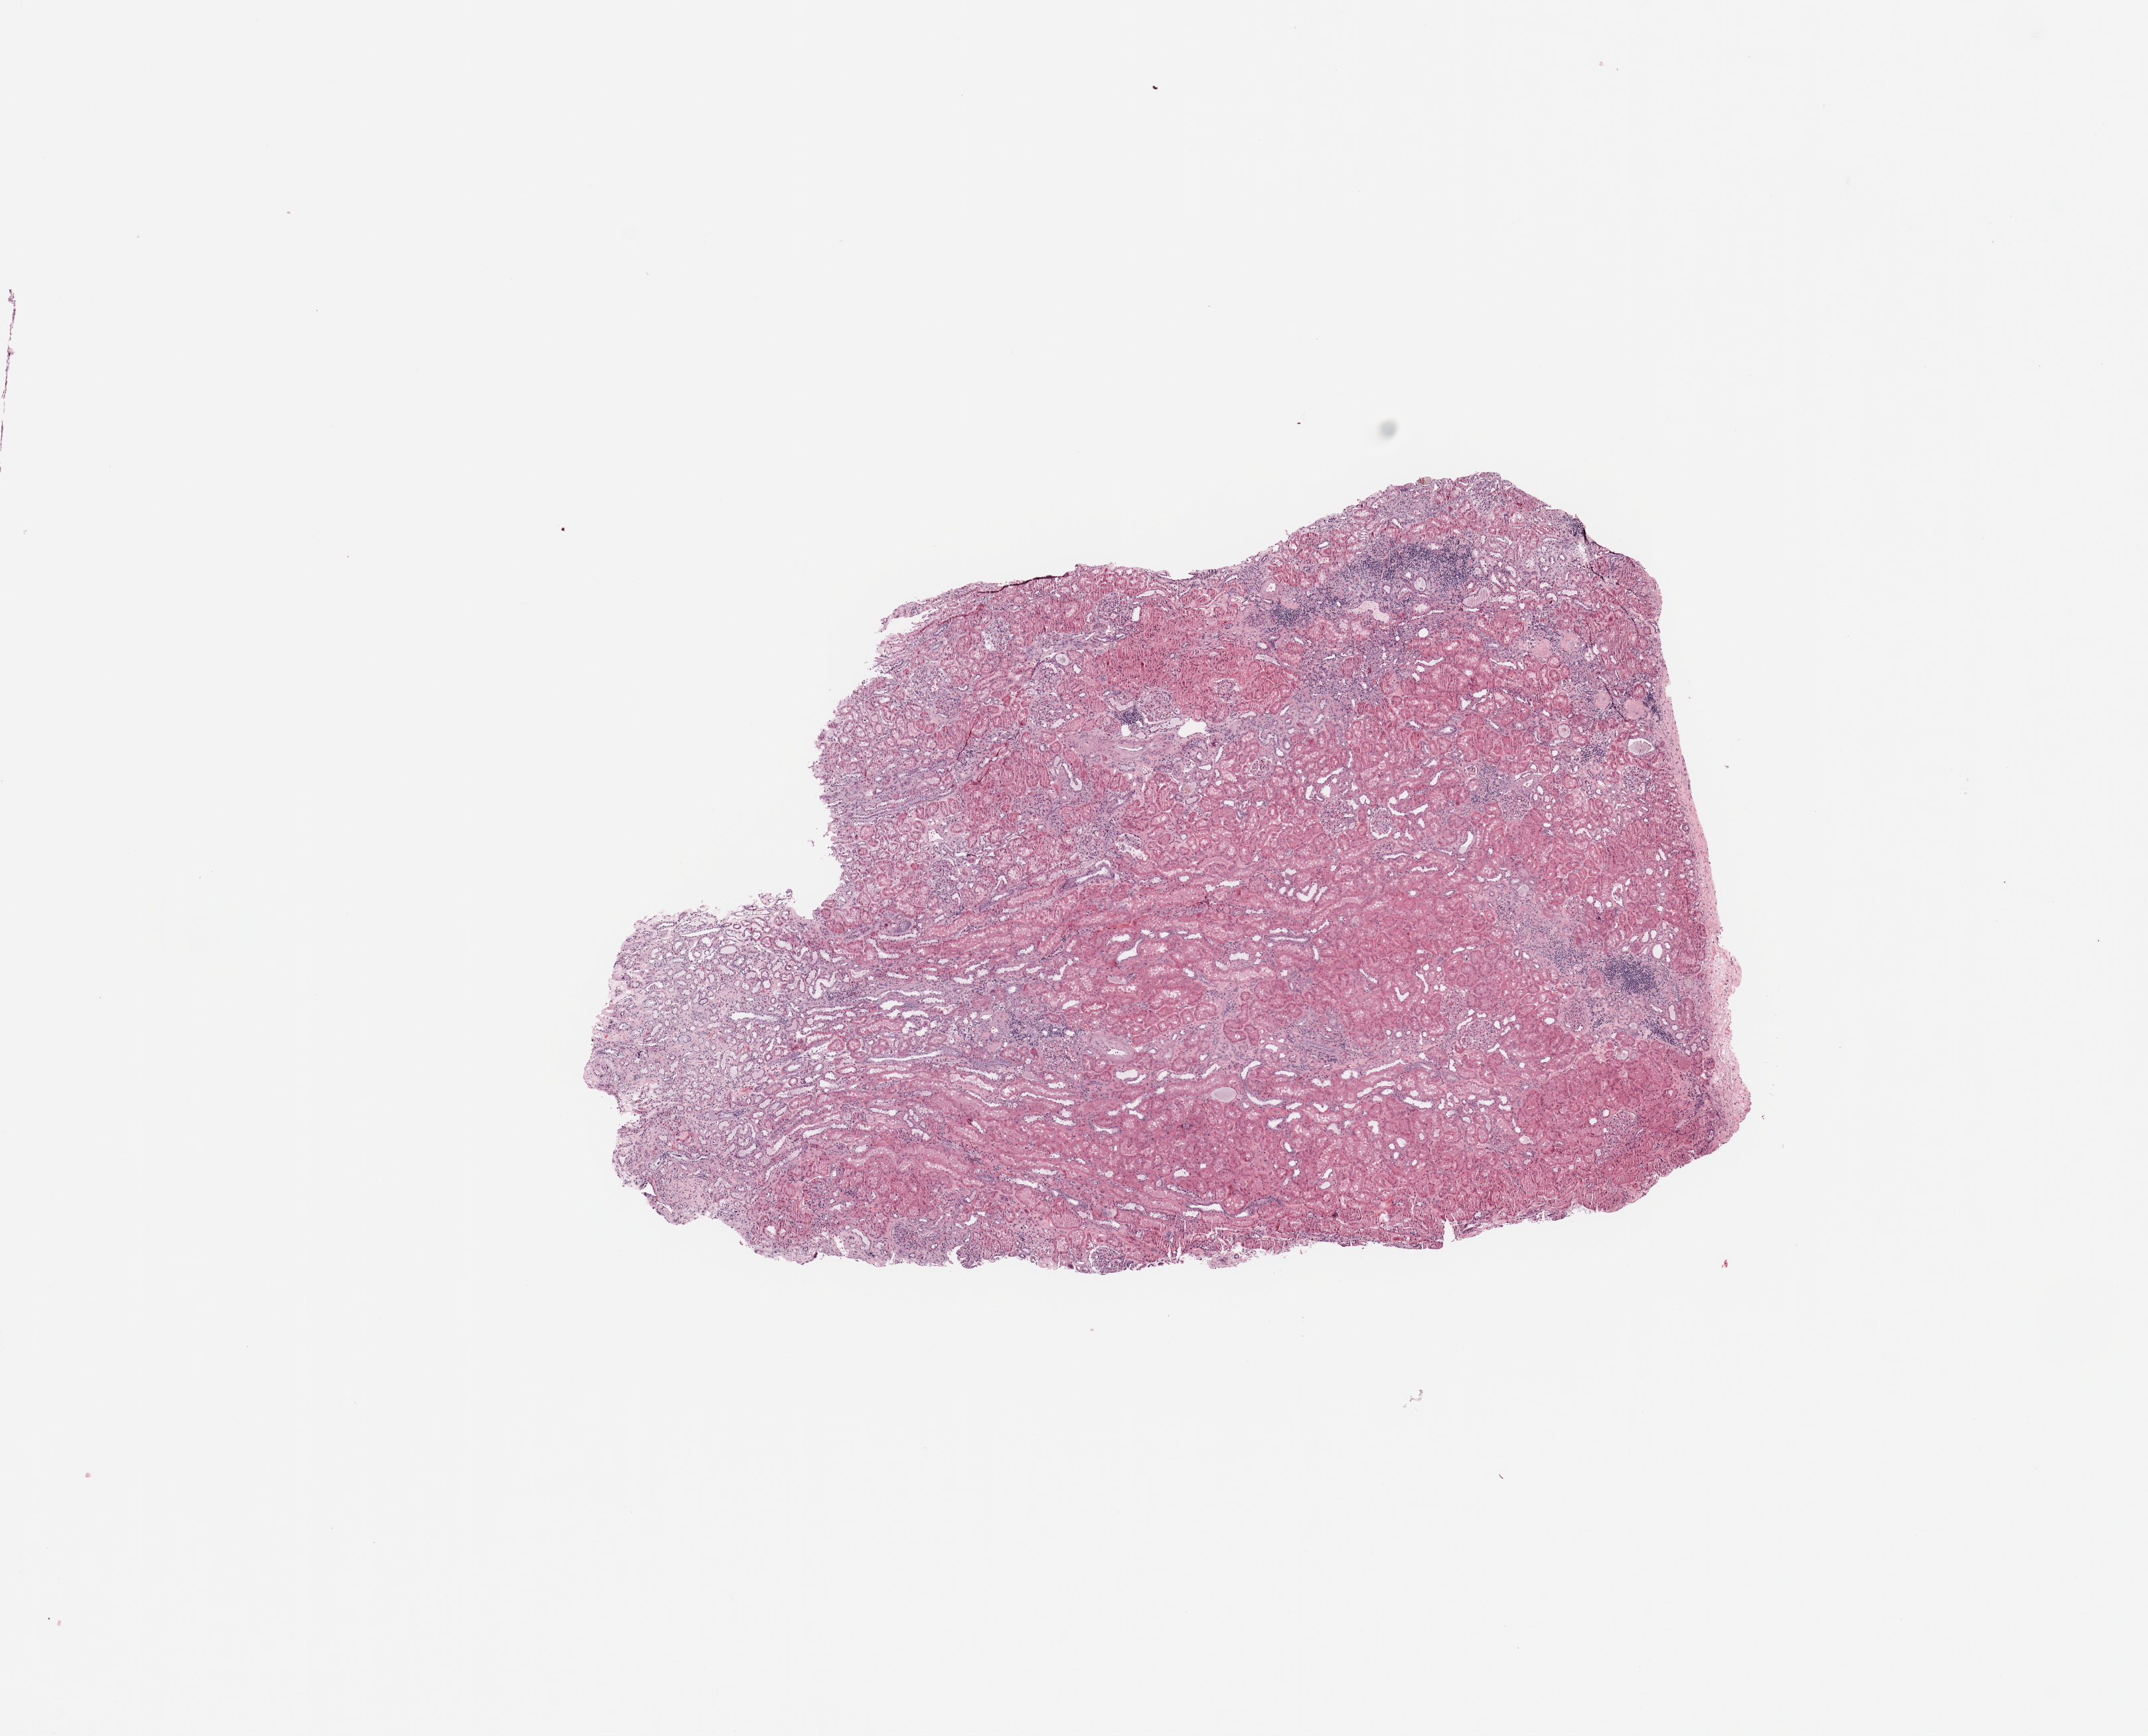
H&E whole-slide image, shown as a low-resolution overview of the whole scanned area (about 12.8 x 10.3 mm, acquisition: 20x scan), normal (non-tumour) tissue sample, sampled site: kidney. Male, 78 y/o.
* this section: normal (non-tumour) tissue from the same patient
* patient diagnosis: Renal cell carcinoma, NOS